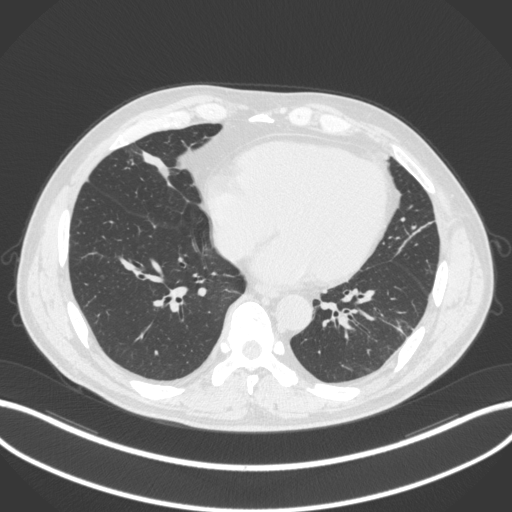
Chest CT, one axial slice; position 90 of 399 along the scan axis; reconstruction kernel B31f; 120 kVp; lung window (W 1500 / L -600 HU); 512 × 512 image matrix. Patient: male, 59 years. From the clinical record (not read from this slice): clinical TNM (as recorded): T2a N1 M0.
Structures marked on this image (rectangle marked by the reading radiologist):
- lung tumour (recorded histology: adenocarcinoma): bounding box <135,146,174,185> (left, top, right, bottom; pixels)